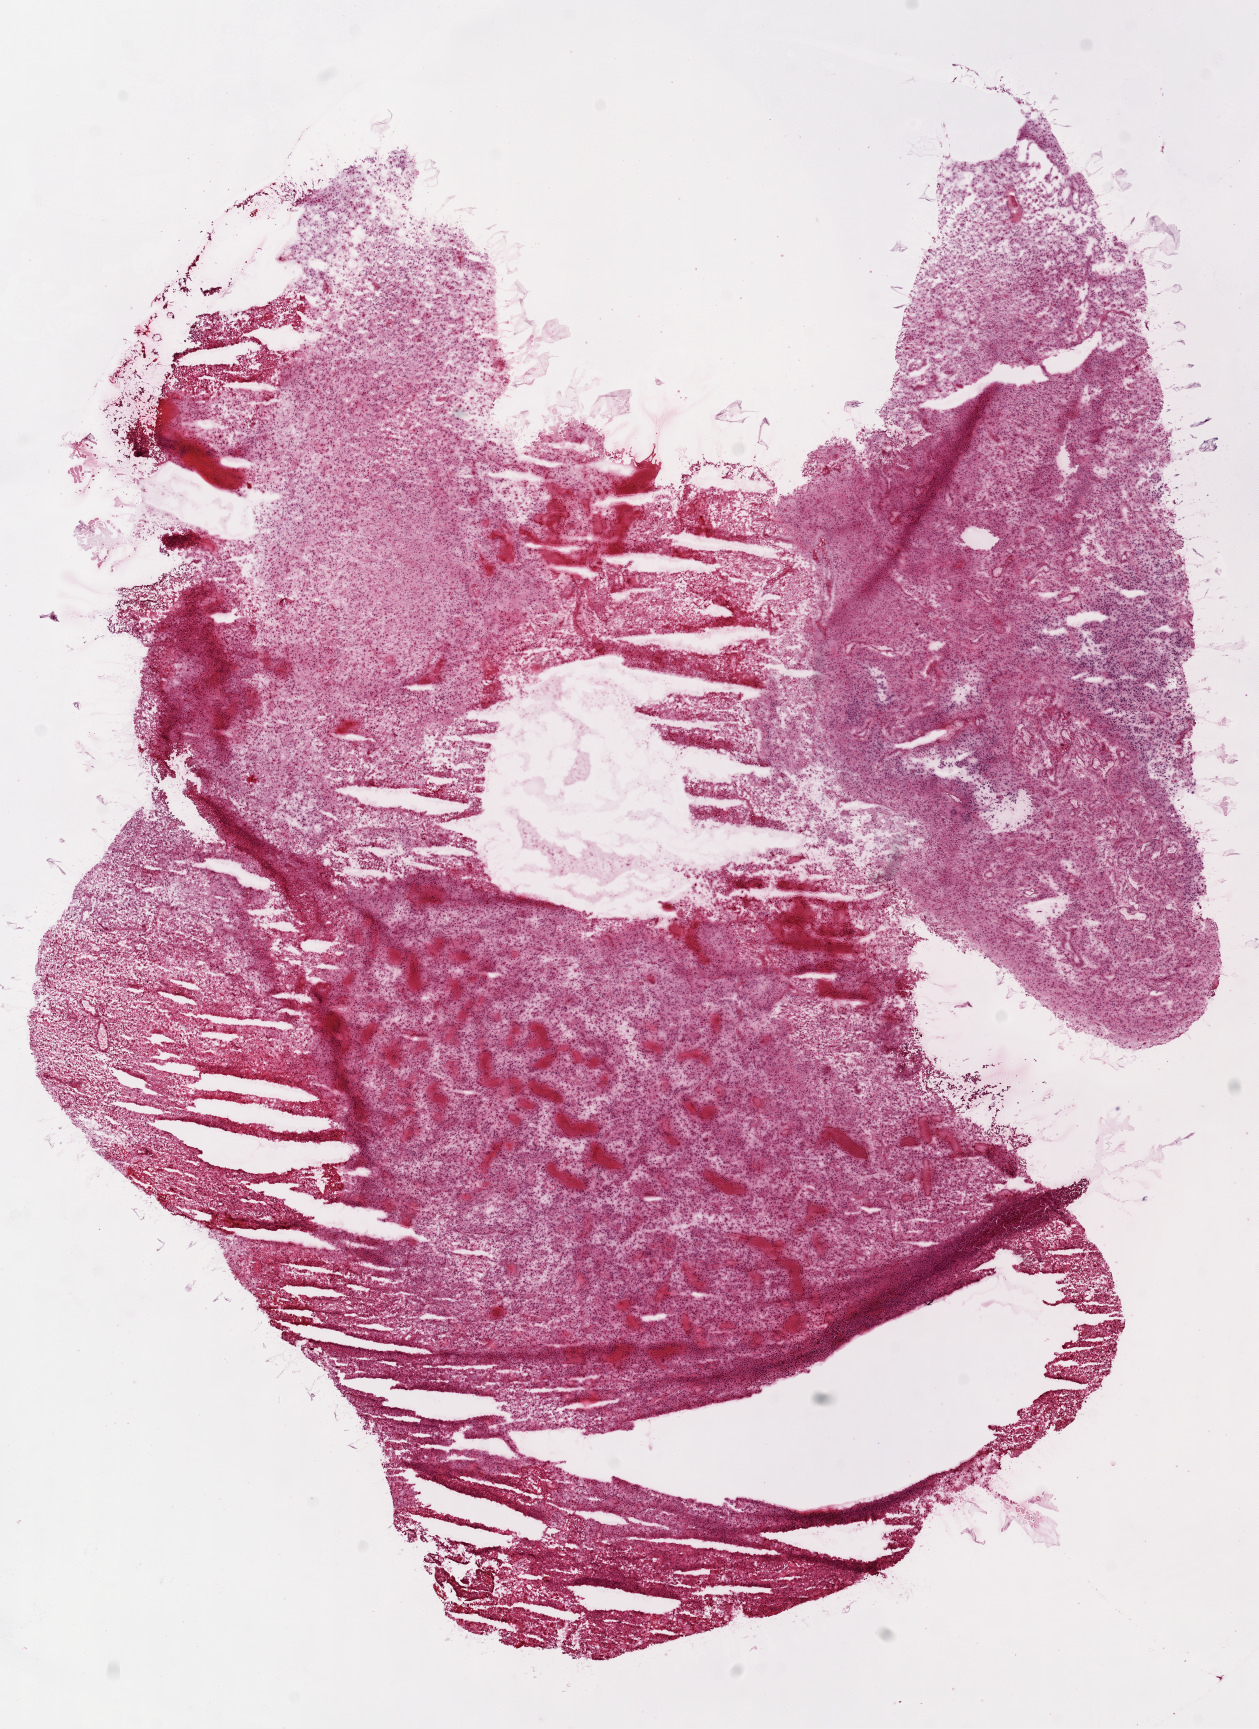
Hematoxylin and eosin (H&E) stained whole-slide image — low-resolution overview of the scanned area, about 10.2 x 13.9 mm (acquisition: 20x scan), frozen section from the top of the tissue portion, primary tumour sample from the brain. Male patient; age at initial diagnosis 46 years. Pathologist review of this section (percent, as recorded): tumour cells 95%, tumour nuclei 100%, normal cells 0%, stromal cells 0%, necrosis 5%.
* pathologic diagnosis: Glioblastoma